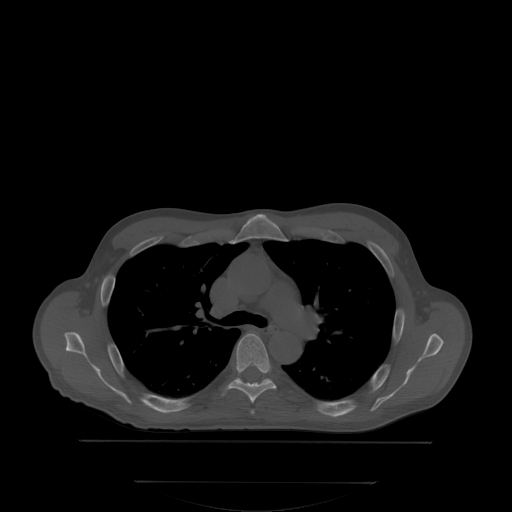
CT including the spine, one axial slice; position 247 of 350 along the scan axis; bone window (W 1800 / L 400 HU); 2.5 mm slice thickness; 512 × 512 image matrix. Patient: male, 58 years. From the clinical record (not read from this slice): primary cancer: prostate; vertebrae with lytic lesions (as recorded): L1.
Outlined on this slice (semi-automatic segmentation, software-assisted and operator-edited):
- T5 vertebra: bounding box (x1, y1, x2, y2) in pixels: (221, 333, 277, 402)